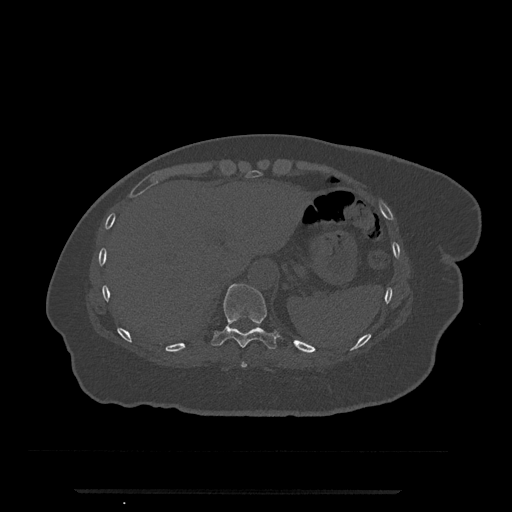
CT including the spine, one axial slice. Slice 286 of 797 in the series (ordered by position). Reconstruction kernel Br40s/3. 120 kVp. Bone window (W 1800 / L 400 HU). 0.5 mm slice thickness. 512 × 512 image matrix. Female patient, age 51 years. Case-level facts recorded for this patient, not image findings: primary cancer: neuro; vertebrae with lytic lesions (as recorded): T8.
Structures marked on this image (semi-automatically segmented with operator editing):
- T10 vertebra: bounding box [x1, y1, x2, y2] px = [211, 284, 278, 349]
- T9 vertebra: [241, 362, 247, 368]